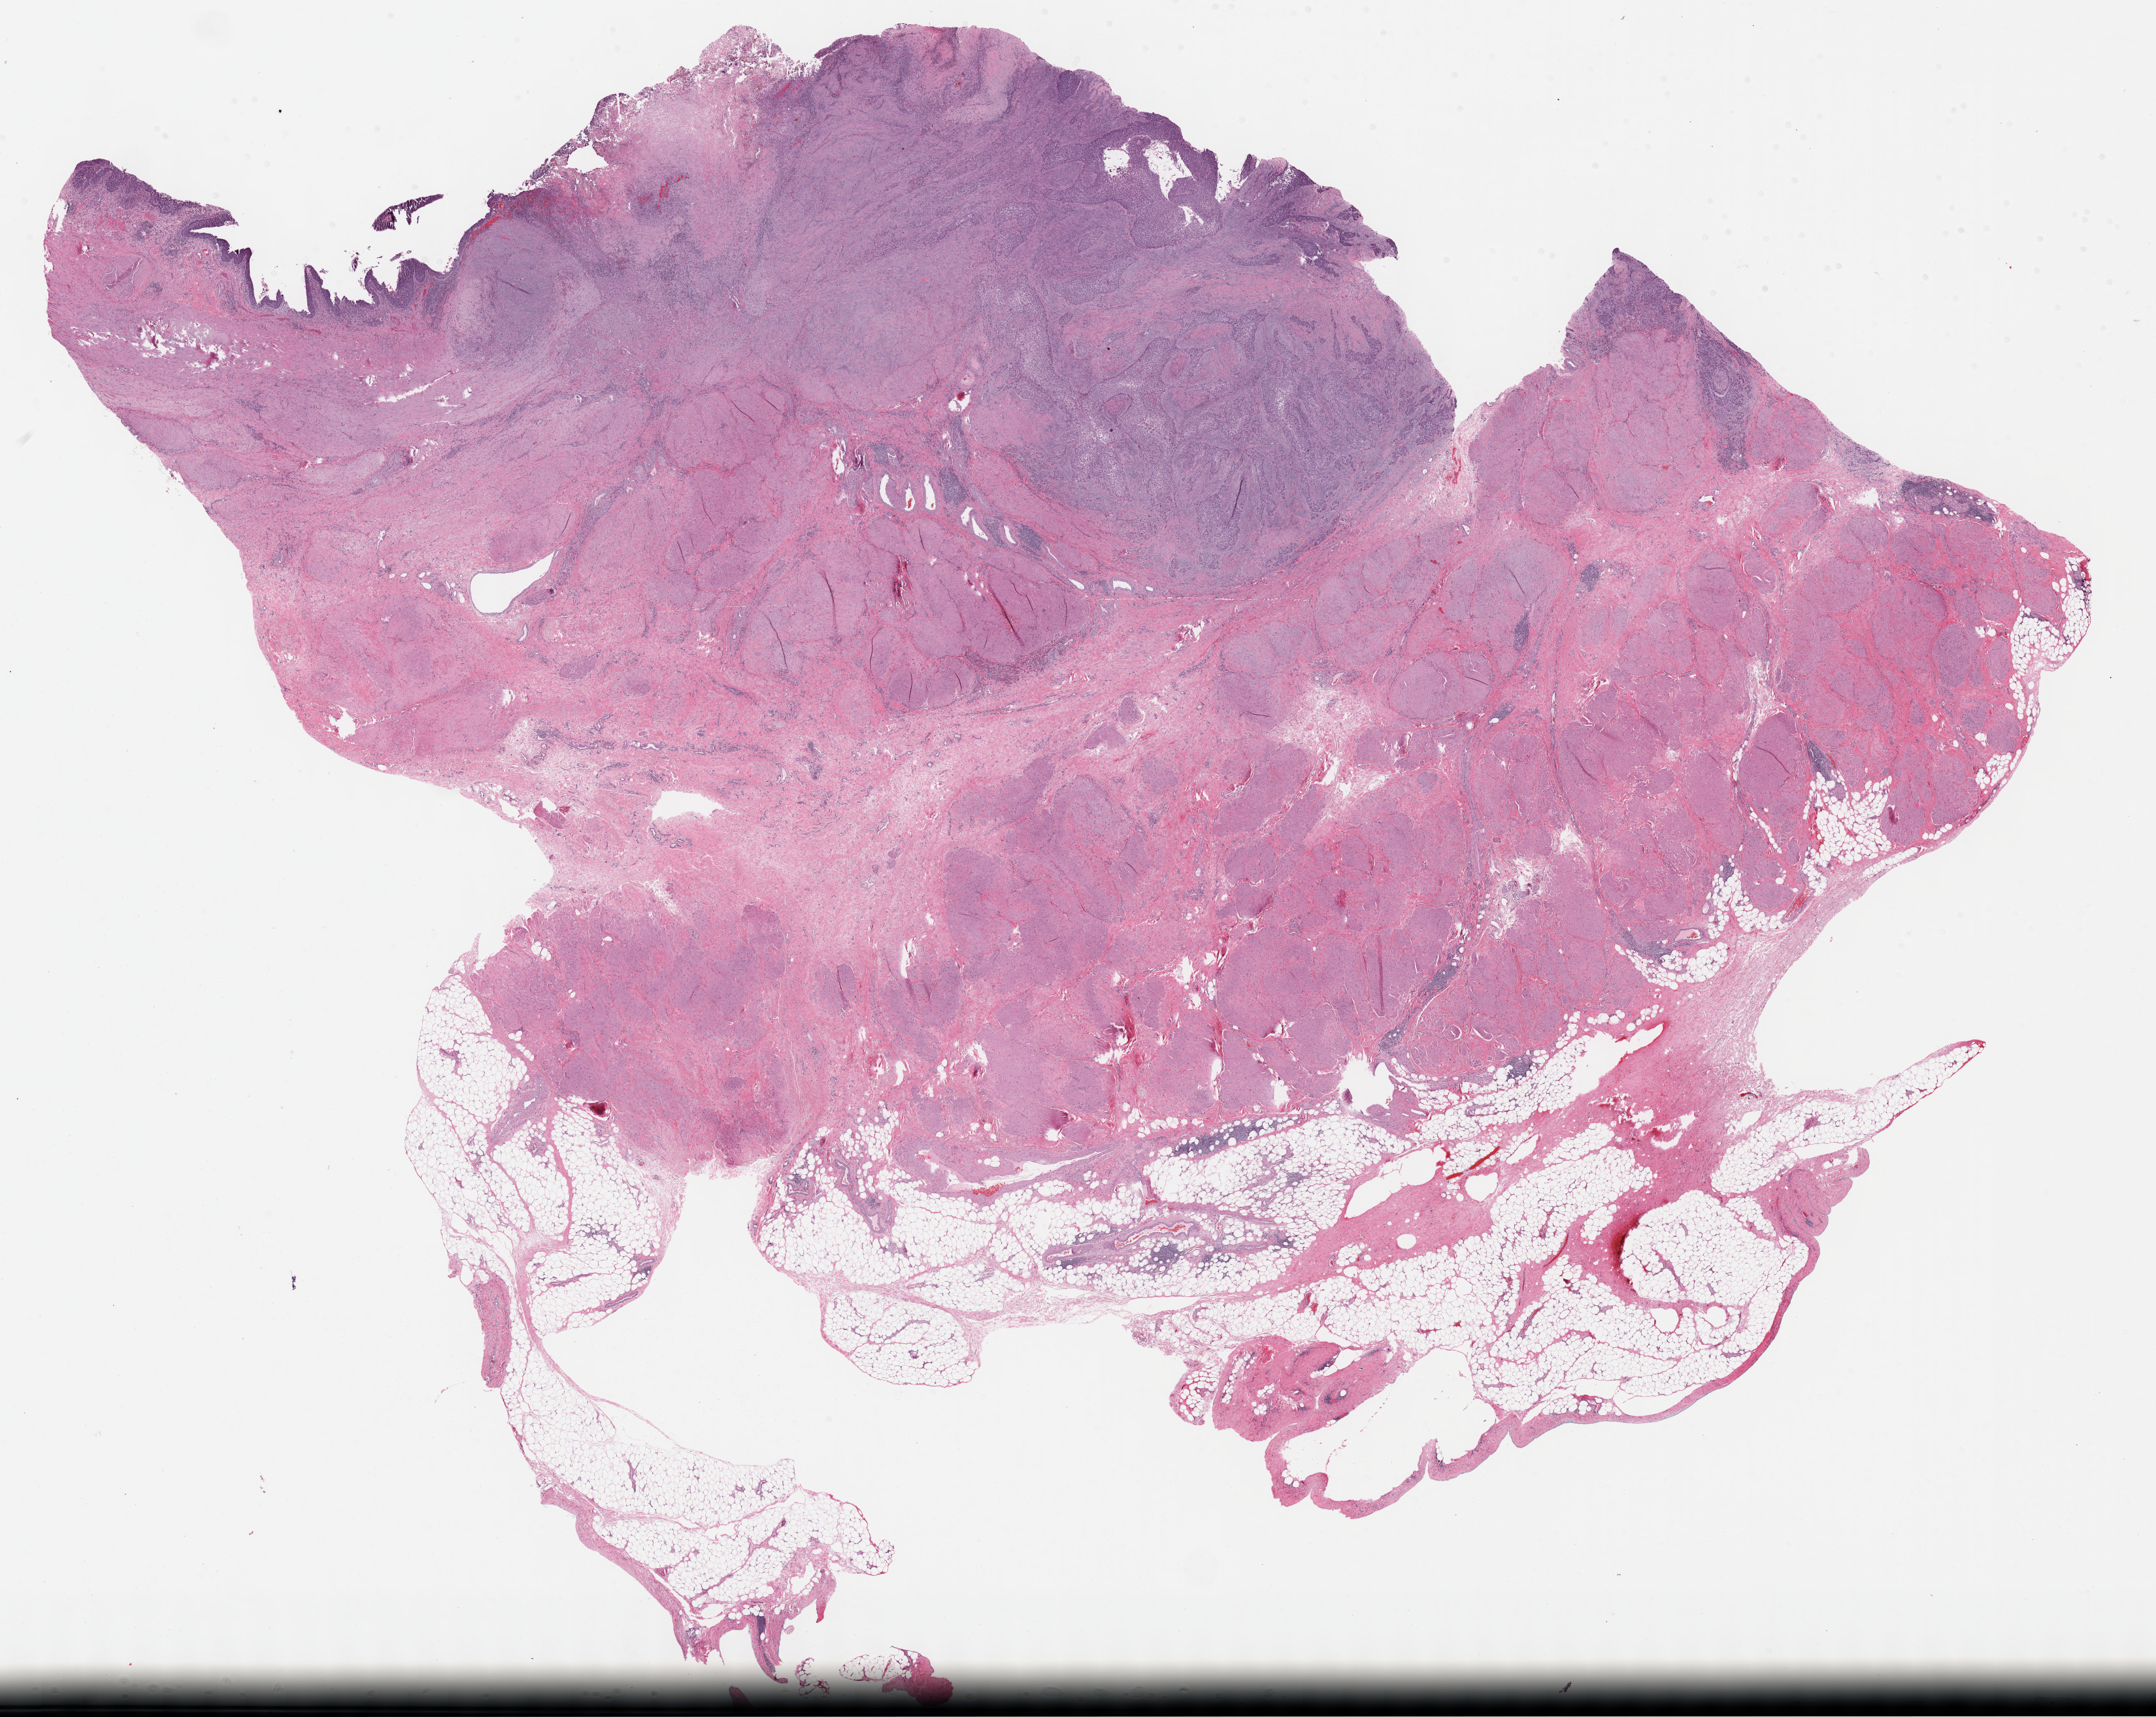
Digitized H&E tissue section (whole slide), a low-resolution overview of the entire scanned area, about 26.7 x 21.3 mm (slide scanned at 40x). FFPE section. Bladder, primary tumour sample. Male patient; age at initial diagnosis 79 years. Histologic grade: high grade.
Lymph nodes positive (case pathology): 0 of 27 examined. TNM: T2b N0 M0. Diagnosis: Transitional cell carcinoma. AJCC pathologic stage: II (6th edition).